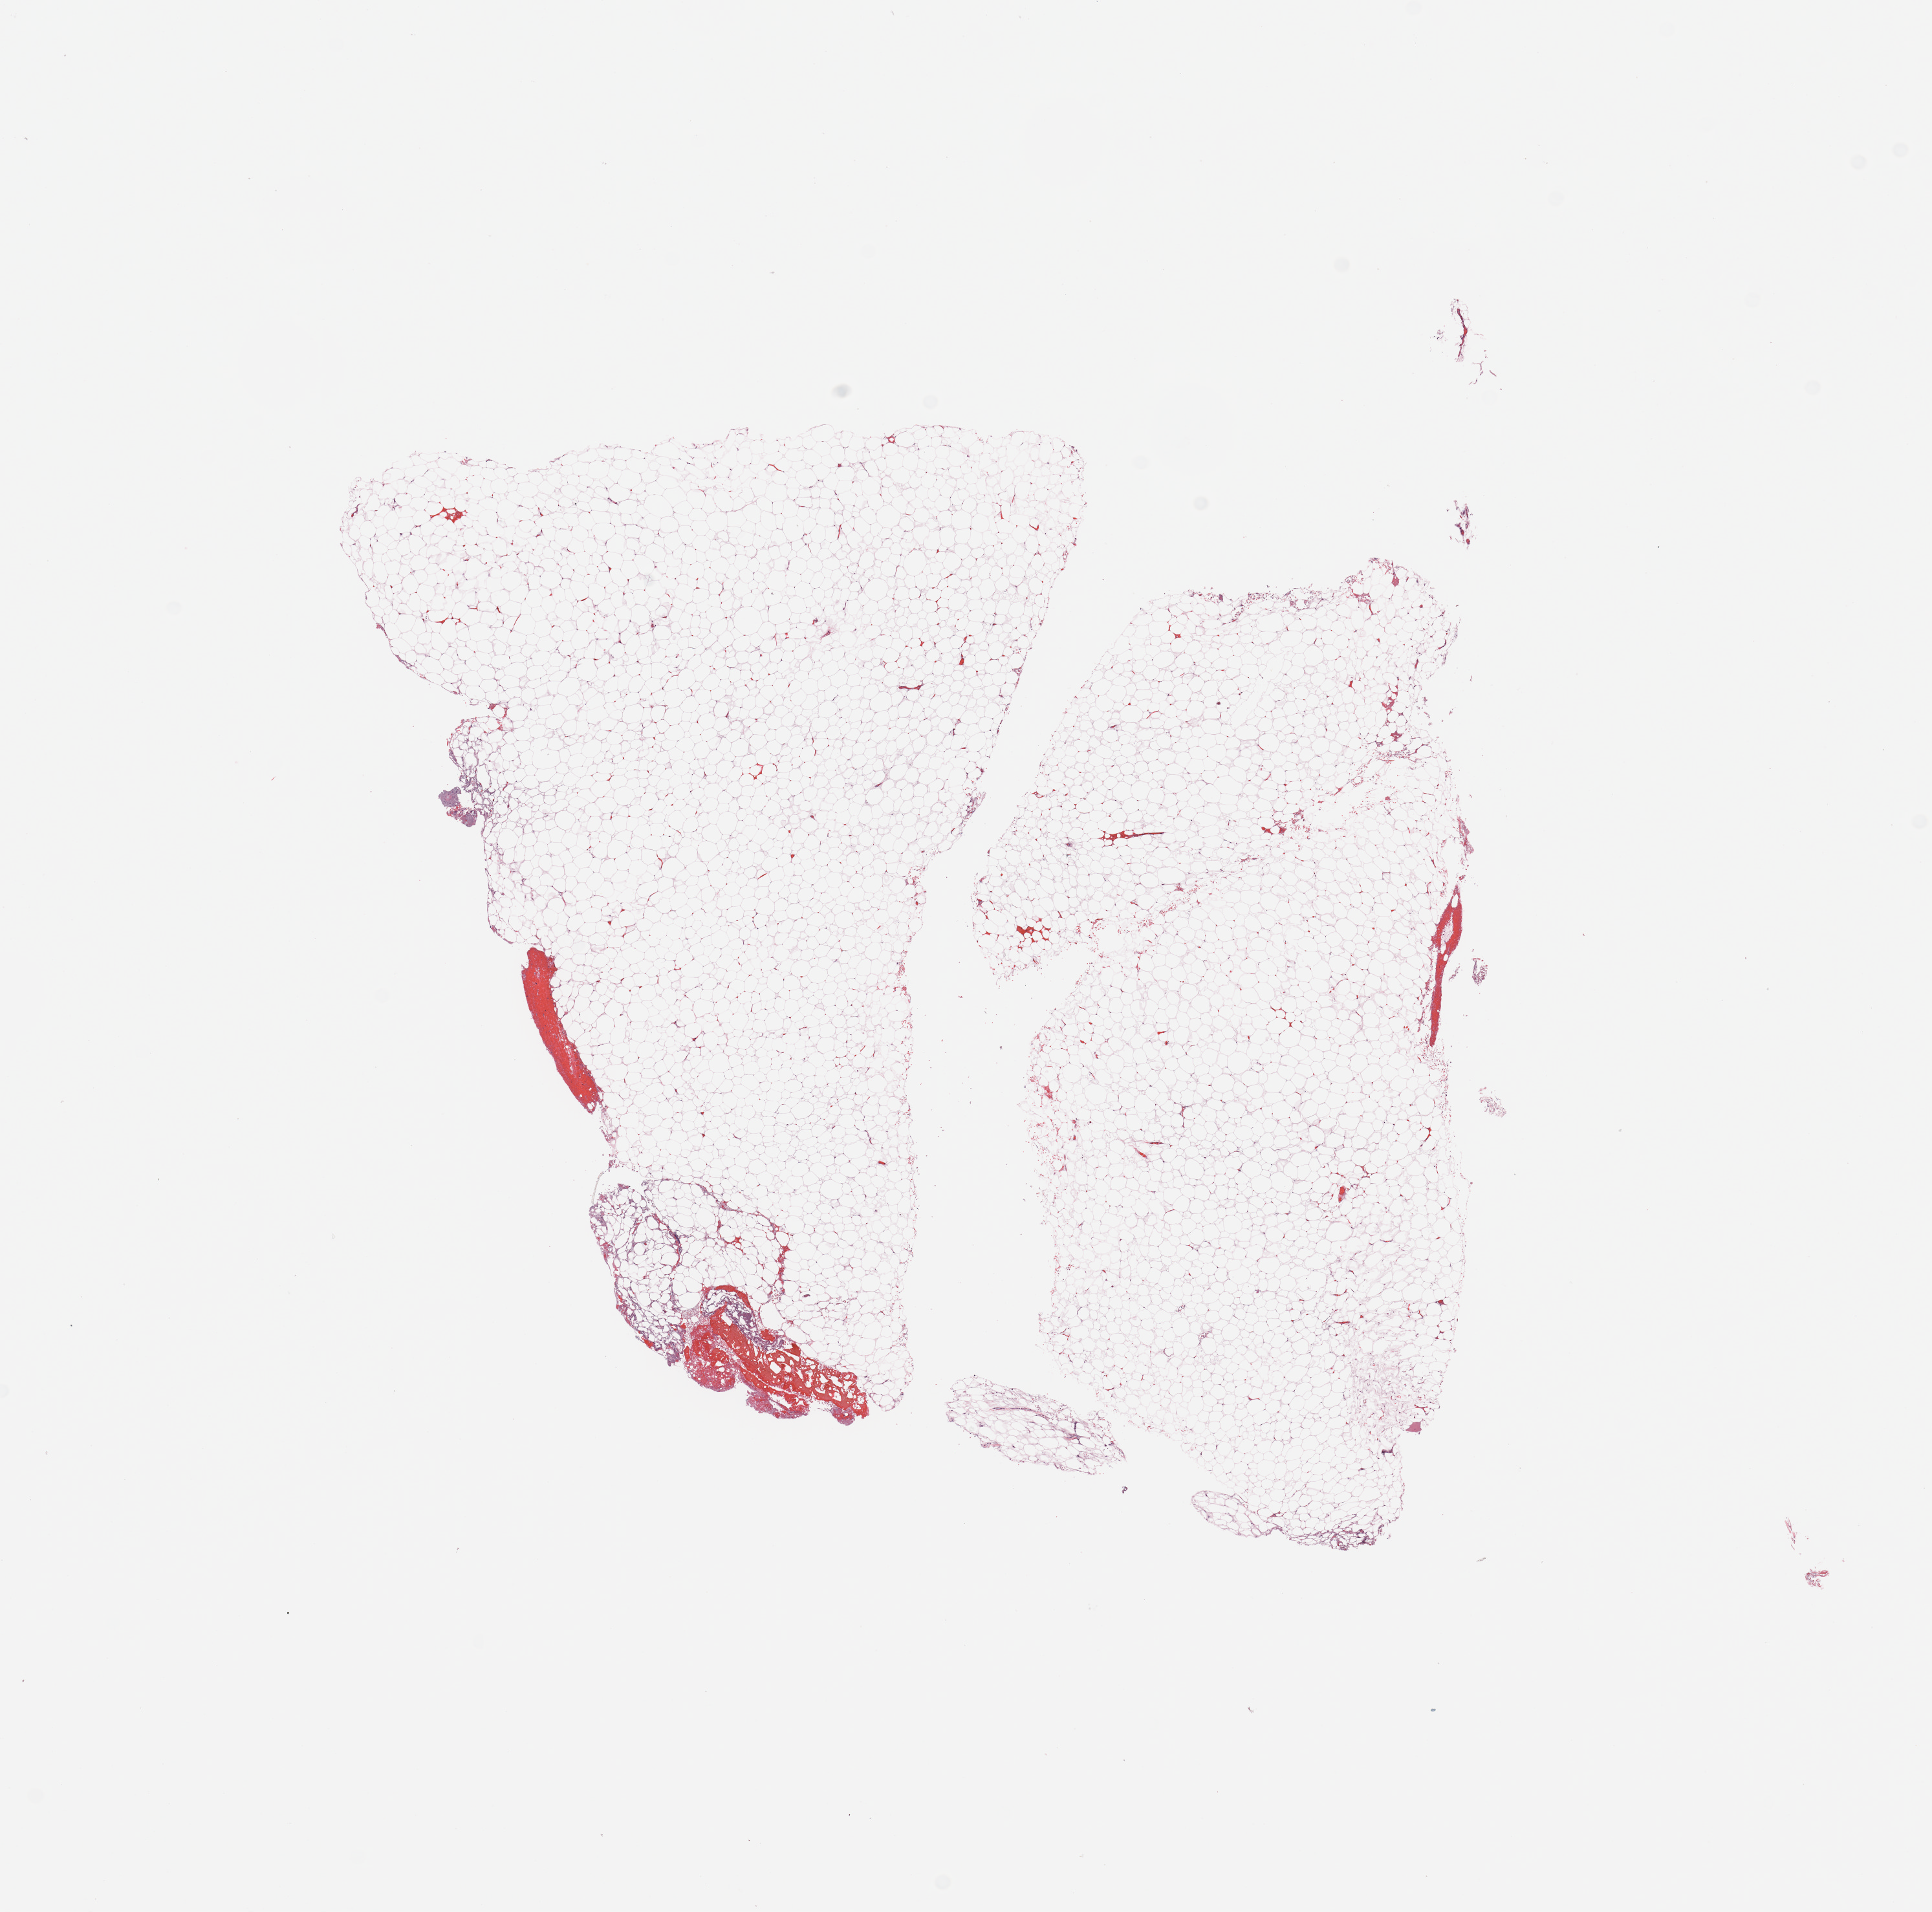
Whole-slide histology image, H&E, a low-resolution overview of the entire scanned area, about 11.8 x 11.7 mm, kidney, normal (non-tumour) tissue. 51-year-old male patient.
This section: normal (non-tumour) tissue from the same patient. Patient diagnosis: Renal cell carcinoma, NOS.